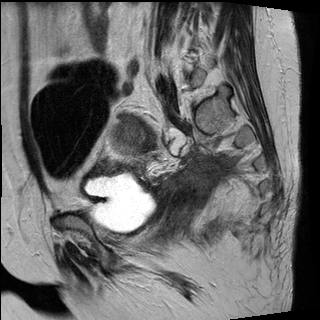
Pelvic MRI for cervical cancer, one sagittal slice. Slice 10 of 30 in the series (ordered by position). T2-weighted. 1.5 T. TE 89 ms, TR 2930 ms. 4 mm slice thickness. 320 × 320 image matrix, field of view 260 × 260 mm. Female patient, age 62 years.
Structures marked on this image (outlined manually by an expert reader):
- uterus and cervix: bounding box [x1, y1, x2, y2] px = [109, 117, 144, 155]